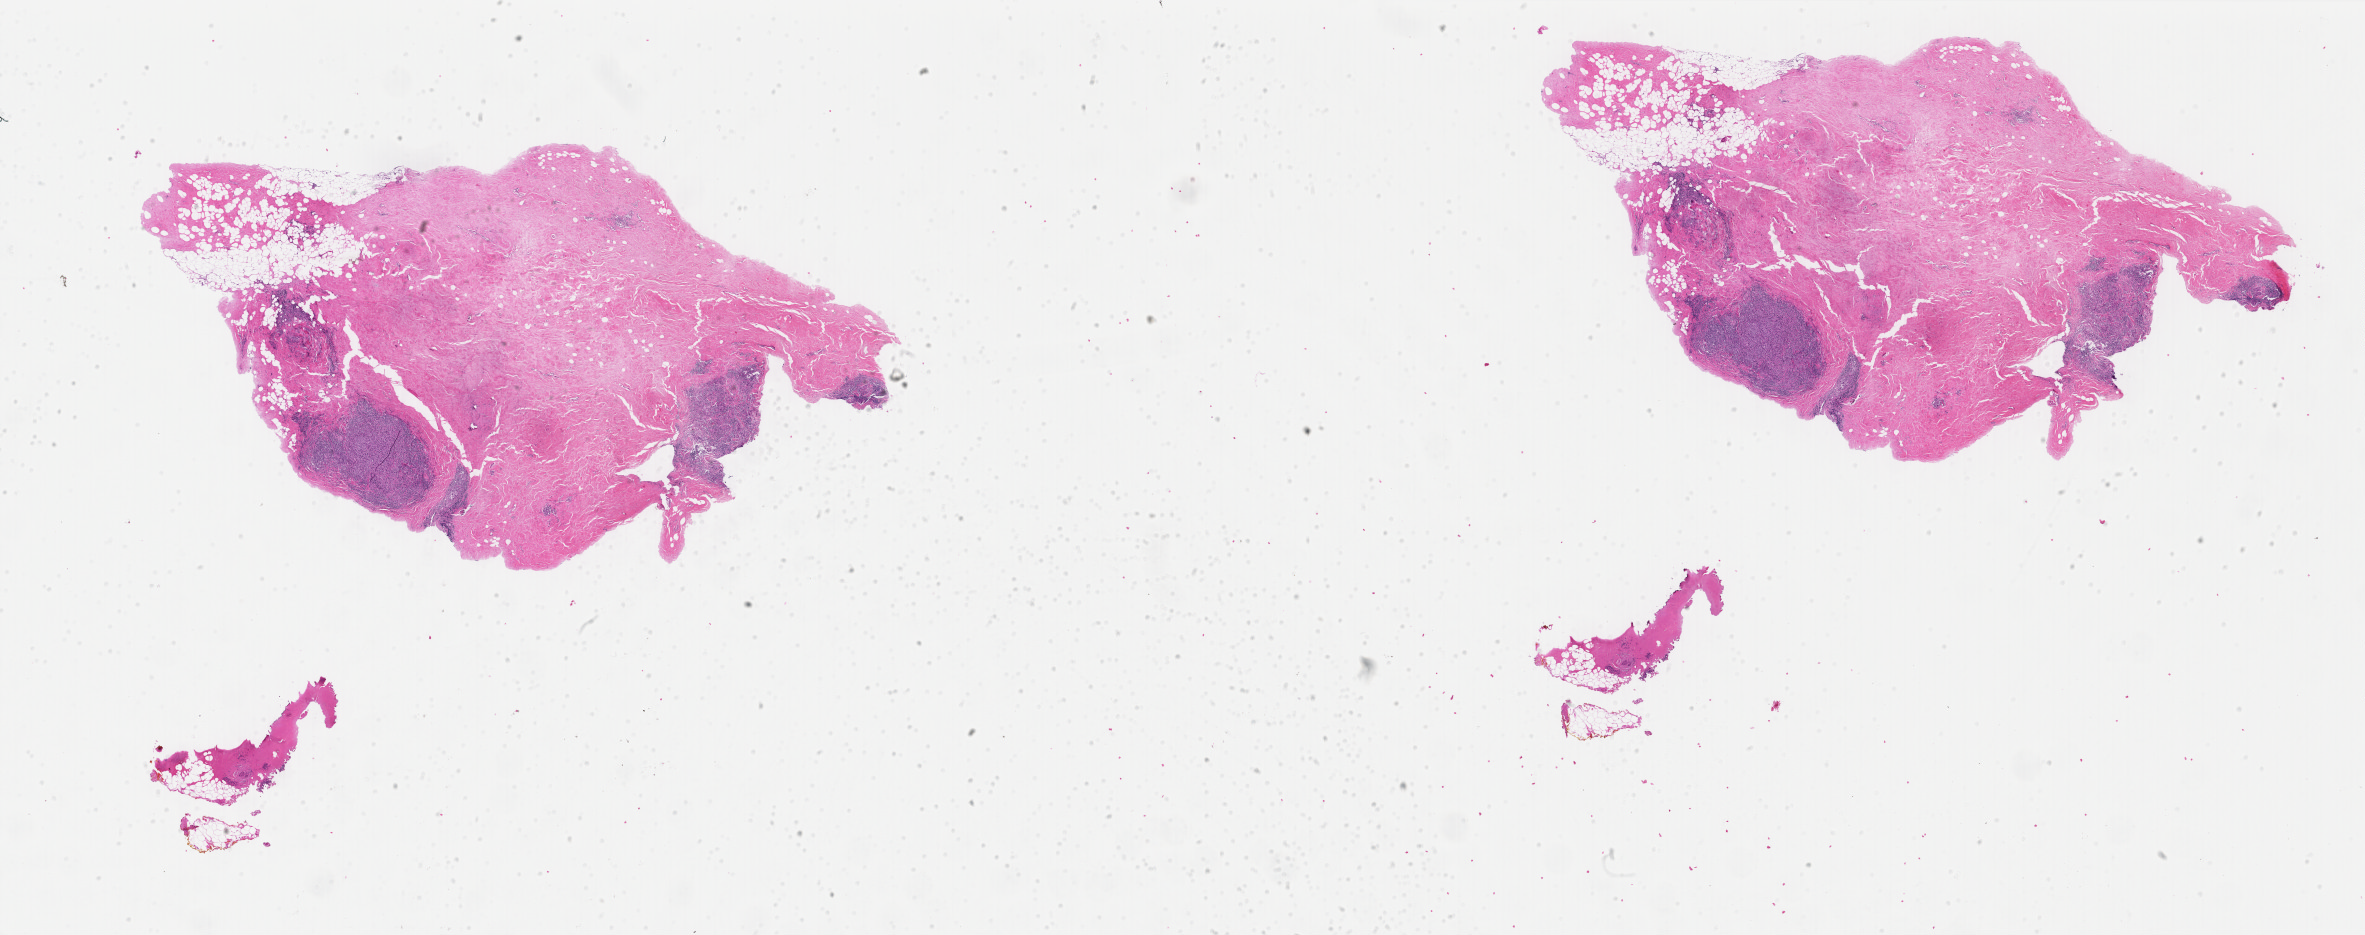
Whole-slide histology image, Hematoxylin and eosin (H&E) stained — low-resolution overview of the scanned area, about 37.5 x 14.8 mm (slide scanned at 40x); FFPE section; breast, primary tumour sample. Patient: female, age at initial diagnosis 62 years.
- AJCC pathologic stage: IIA (6th edition)
- pathologic diagnosis: Infiltrating duct carcinoma, NOS
- laterality: right
- lymph nodes positive (case pathology): 3 of 9 examined